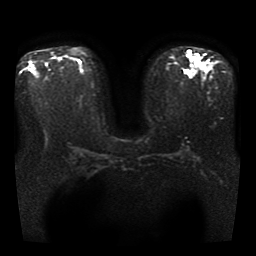
Breast MRI, one axial slice; position 23 of 40 along the scan axis; diffusion-weighted series; image 2 of 4 stored at this slice position (different b-values; order by instance number); 1.5 T; 5 mm slice thickness; 256 × 256 image matrix, field of view 330 × 330 mm. Female patient.
Structures marked on this image (manually delineated by an expert):
- tumour on diffusion-weighted imaging: box from (x=187, y=50) to (x=205, y=70) px